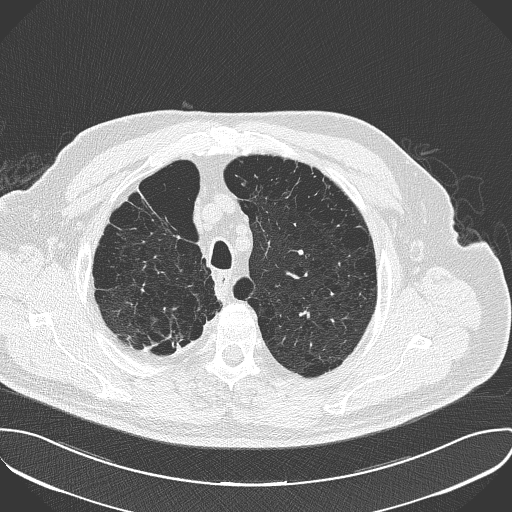
Axial slice from a low-dose chest CT screening exam; baseline annual screen; lung window (W 1500 / L -600 HU); 2 mm slice thickness; lung (sharp) reconstruction kernel (B50f); slice 36 of 181 in the series; 512 × 512 image matrix. Male participant, aged 68 years at enrolment. Current smoker at enrolment.
Lesion marked by an expert reader, bounding box <124,323,197,366> (left, top, right, bottom; pixels). The screening reader recorded 3 non-calcified nodules or masses ≥4 mm on this exam (left lower lobe, left upper lobe, right lower lobe); which of them this box marks is not recorded. Later outcome: lung cancer diagnosed 661 days after this screen (after the second annual screen) — adenocarcinoma, NOS, right upper lobe, stage IV (AJCC 6th edition), 29 mm at pathology.